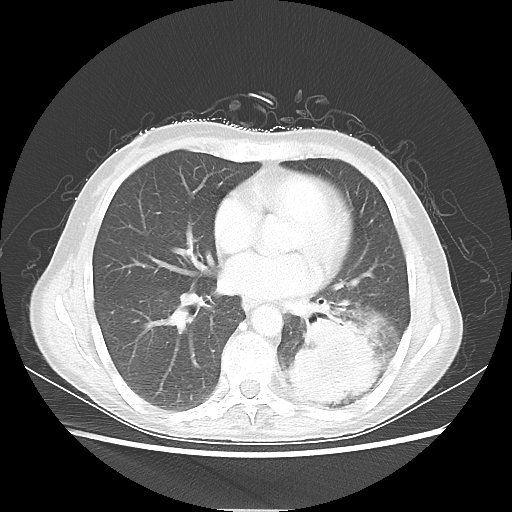
Chest CT, one axial slice. Position 26 of 56 along the scan axis. 80 kVp. Lung window (W 1500 / L -600 HU). 512 × 512 image matrix, field of view 360 × 360 mm. Female patient, age 53 years. From the clinical record (not read from this slice): clinical TNM (as recorded): T3 N0 M0.
Structures marked on this image (rectangle marked by the reading radiologist):
- lung tumour (recorded histology: adenocarcinoma): bounding box [x1, y1, x2, y2] px = [287, 319, 381, 406]